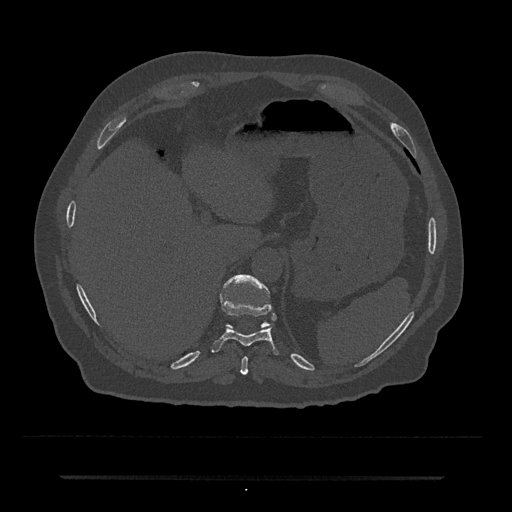
CT including the spine, one axial slice; slice 224 of 797 in the series (ordered by position); reconstruction kernel Br40s/3; 120 kVp; bone window (W 1800 / L 400 HU); 0.5 mm slice thickness; 512 × 512 image matrix. Male patient, age 69 years. Case-level facts recorded for this patient, not image findings: primary cancer: prostate.
Annotated regions visible in this slice (semi-automatic segmentation, software-assisted and operator-edited):
- T10 vertebra: box from (x=211, y=301) to (x=279, y=355) px
- T11 vertebra: (x=221, y=274)–(x=270, y=328)
- T9 vertebra: (x=240, y=356)–(x=248, y=375)